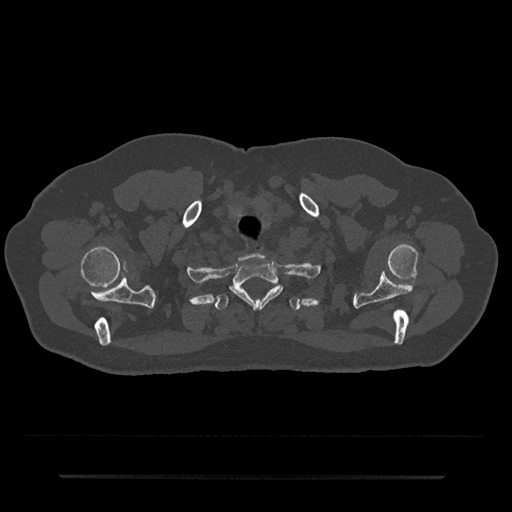
CT including the spine, one axial slice. Slice 634 of 797 in the series (ordered by position). Bone window (W 1800 / L 400 HU). 512 × 512 image matrix, field of view 437 × 437 mm. Male patient, age 69 years. From the clinical record (not read from this slice): primary cancer: prostate.
Outlined on this slice (semi-automatic segmentation, software-assisted and operator-edited):
- T1 vertebra: bounding box <230,261,282,307> (left, top, right, bottom; pixels)
- T2 vertebra: <215,287,300,311>